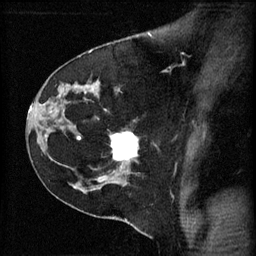
Breast MRI (dynamic contrast-enhanced), one sagittal slice. Position 40 of 60 along the scan axis. 3 images stored at this slice position (order not interpretable as contrast timing). 1.5 T. TE 4.2 ms, TR 11 ms. 256 × 256 image matrix, field of view 180 × 180 mm. Female patient, age 45 years.
Structures marked on this image (semi-automatically segmented with operator editing):
- analysis volume of interest (the breast-tissue region the enhancement analysis was run in; not a lesion): bounding box [x1, y1, x2, y2] px = [112, 130, 141, 171]
- tumour enhancement mask (voxels above the 70 % enhancement threshold inside the analysis volume of interest): [112, 132, 139, 169]